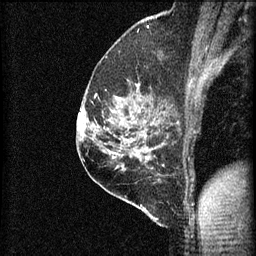
Breast MRI (dynamic contrast-enhanced), one sagittal slice; position 41 of 60 along the scan axis; 3 images stored at this slice position (order not interpretable as contrast timing); 1.5 T; TE 4.2 ms, TR 8.2 ms; 2 mm slice thickness; 256 × 256 image matrix, field of view 180 × 180 mm. Female patient, age 59 years.
Annotated regions visible in this slice (semi-automatically segmented with operator editing):
- analysis volume of interest (the breast-tissue region the enhancement analysis was run in; not a lesion): box from (x=92, y=78) to (x=155, y=131) px
- tumour enhancement mask (voxels above the 70 % enhancement threshold inside the analysis volume of interest): (x=117, y=96)–(x=119, y=99)